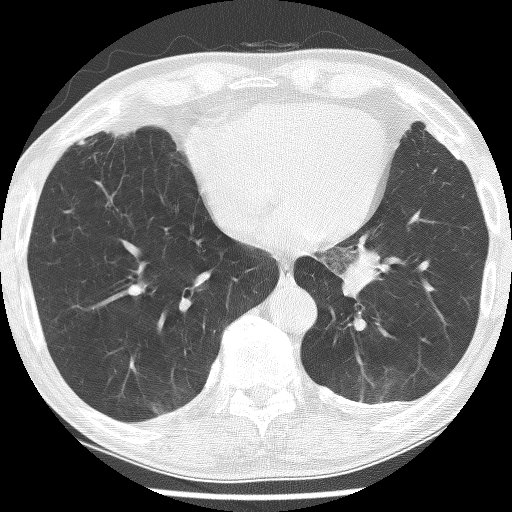
Chest CT (low-dose screening protocol), one axial image. Baseline screening round. Lung window (W 1500 / L -600 HU). Lung (sharp) reconstruction kernel (BONE). 512 × 512 image matrix, field of view 320 × 320 mm. Male, age 74 years at enrolment. Current smoker at enrolment.
Lesion marked by an expert reader, bounding box (x1, y1, x2, y2) in pixels: (318, 229, 425, 322). Reader record for this screening exam (exam-level; its link to the box is not recorded): non-calcified nodule or mass ≥4 mm, left lower lobe, 30 × 27 mm, spiculated (stellate) margins, soft tissue attenuation. Participant outcome: lung cancer diagnosed 151 days after this screen — adenocarcinoma, NOS, left lower lobe, stage IIIA (AJCC 6th edition), 49 mm at pathology.